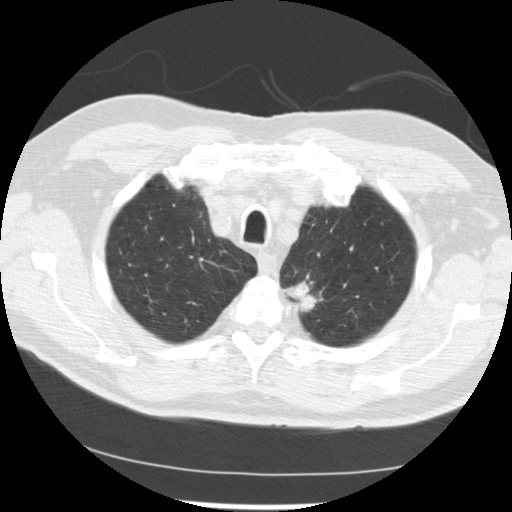
Axial slice from a low-dose chest CT screening exam; baseline annual screen; lung window (W 1500 / L -600 HU); 2.5 mm slice thickness. Male, age 71 years at enrolment. Current smoker at enrolment.
Lesion marked by an expert reader, box from (x=271, y=270) to (x=337, y=319) px. The screening reader recorded 2 non-calcified nodules or masses ≥4 mm on this exam (left upper lobe, left upper lobe); which of them this box marks is not recorded.